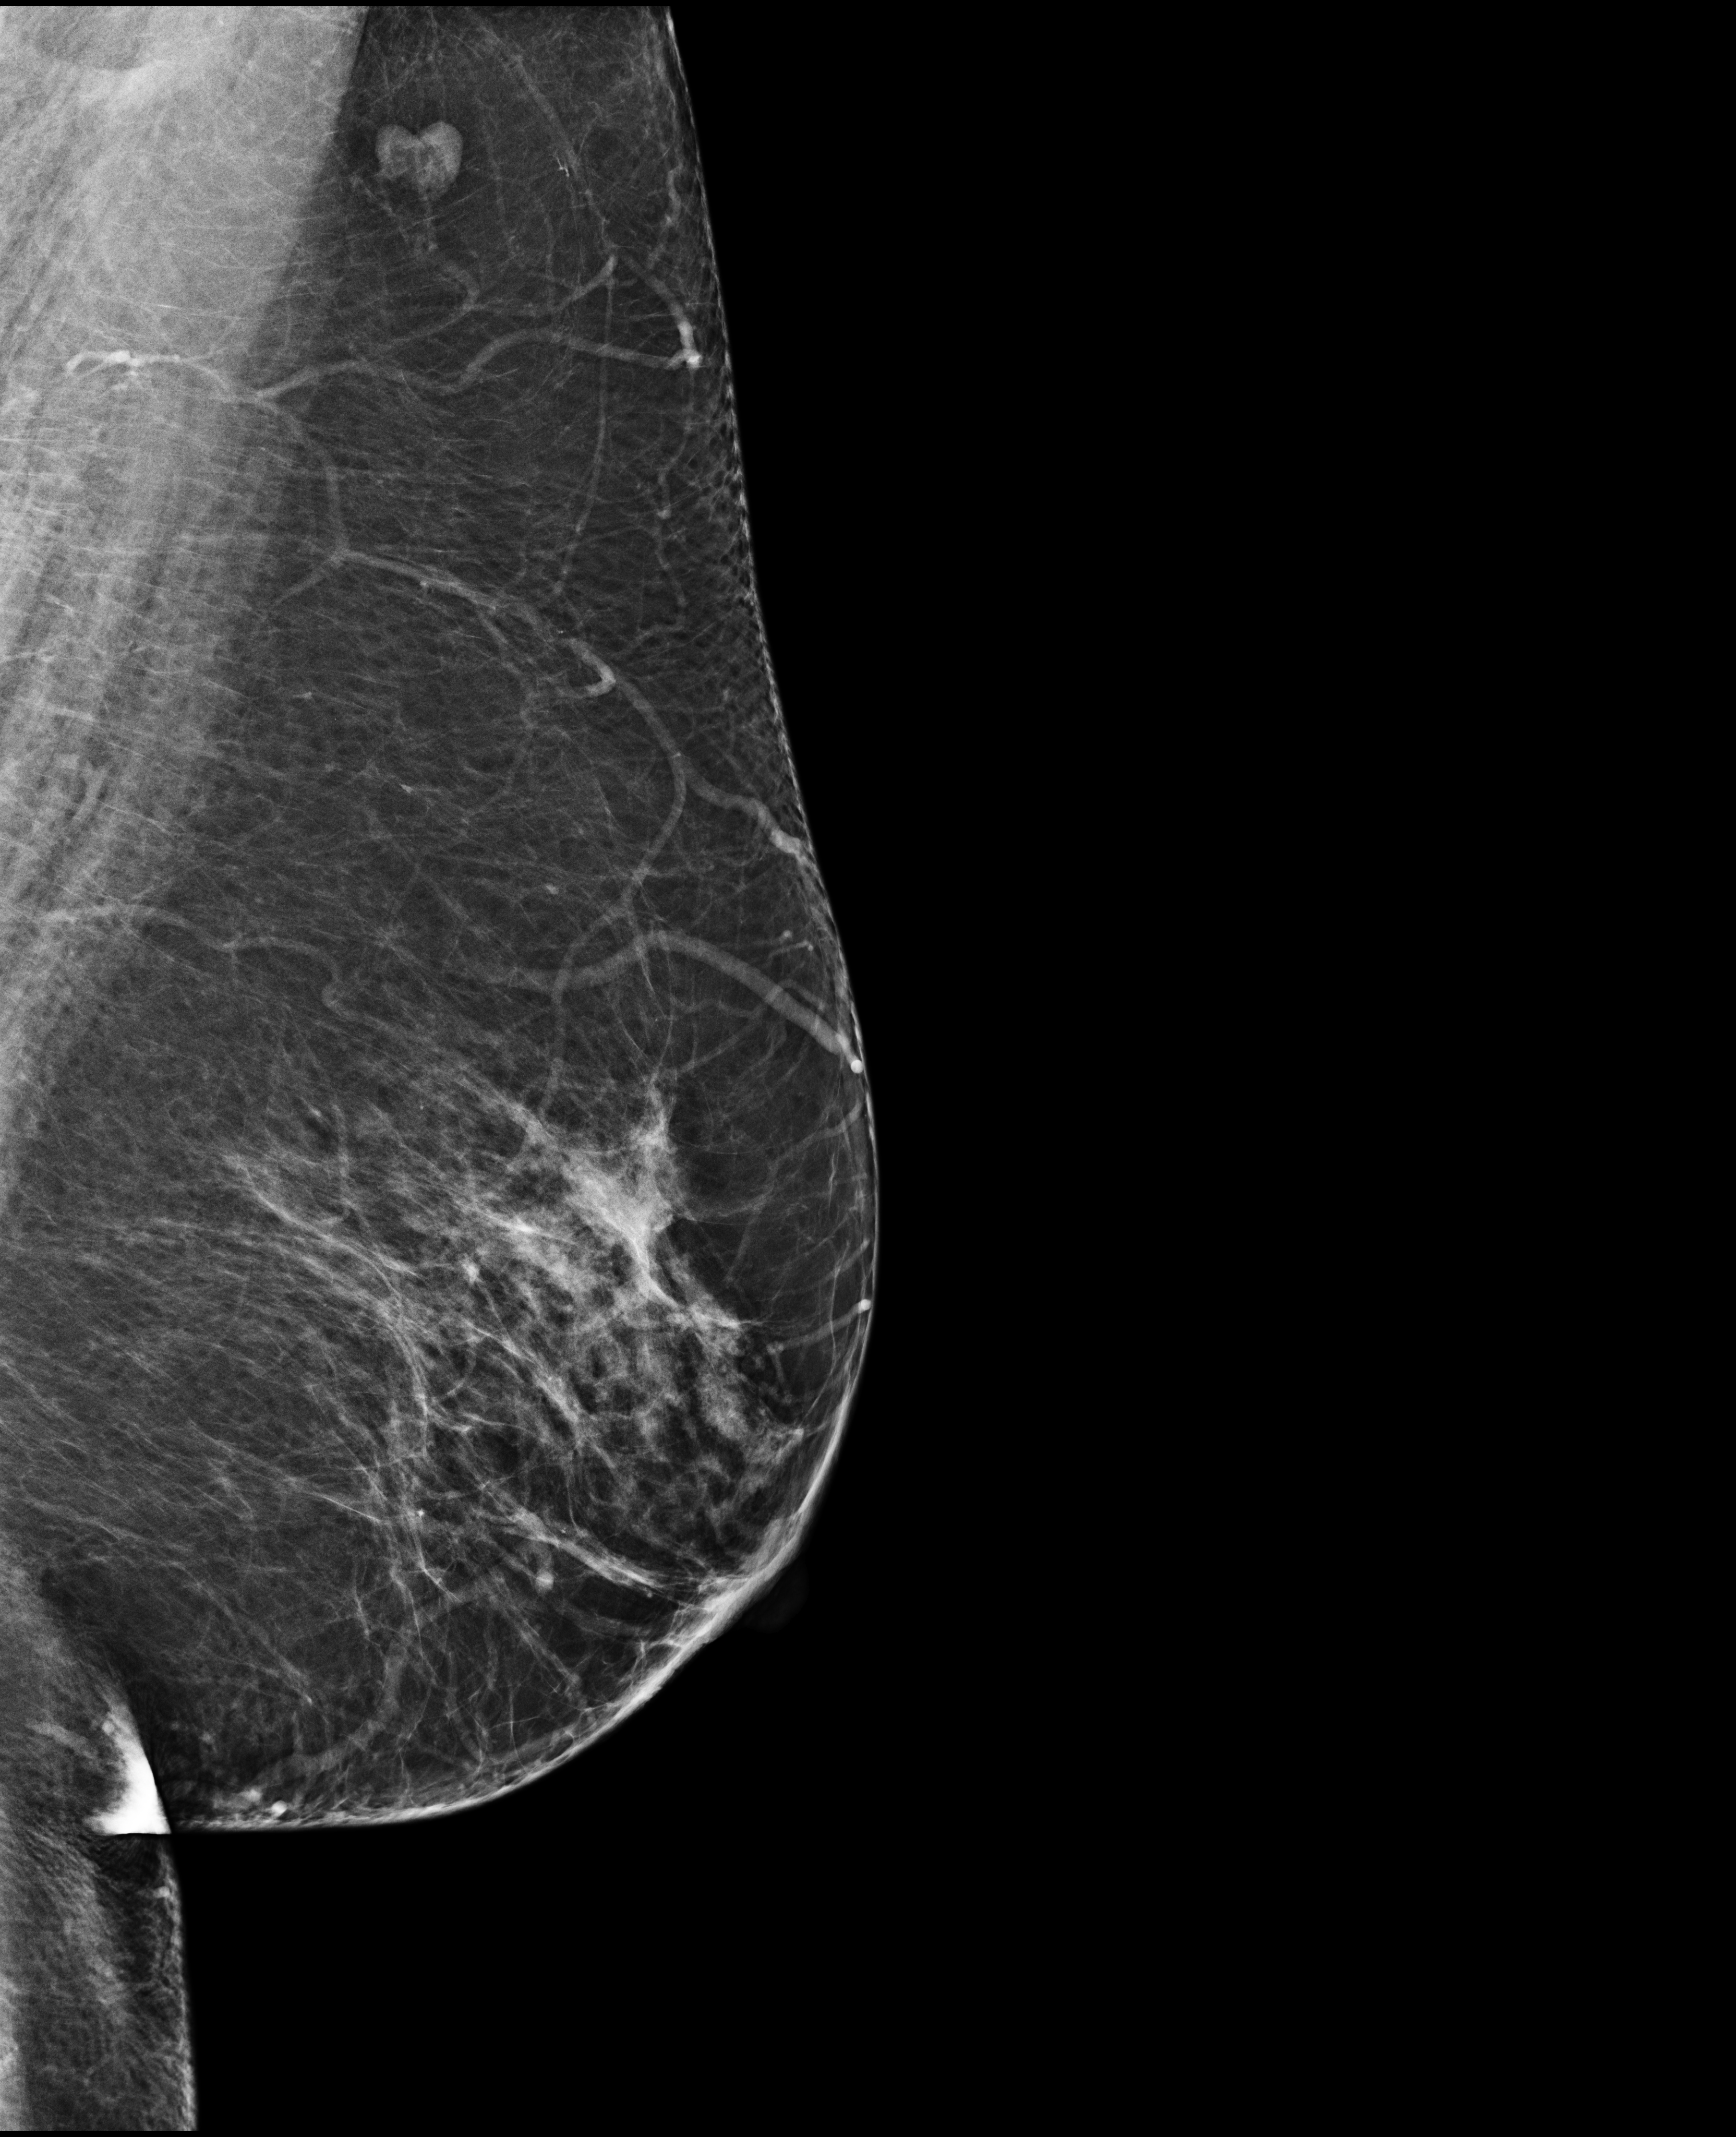
Full-field digital mammogram (FFDM), left breast, MLO view, annual screening mammography examination, system: Selenia Dimensions. Patient: female, 61 years.
Breast density at the screening exam (both breasts): heterogeneously dense (BI-RADS density category c). Final BI-RADS category for the screening round (tomosynthesis exam, both breasts): category 1. Recall: no recall after this screen.